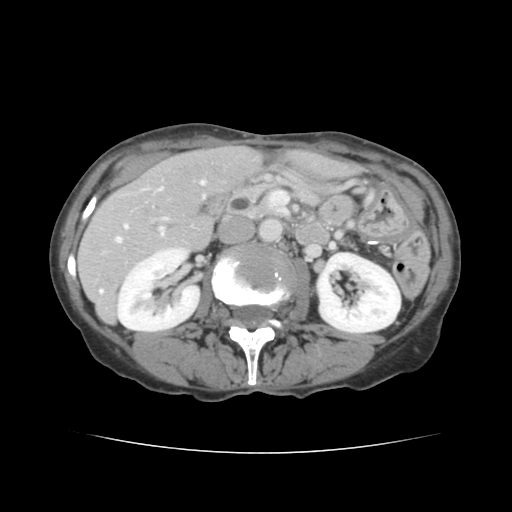
Contrast-enhanced abdominal CT, one axial slice. Position 60 of 136 along the scan axis. Intravenous contrast given. Soft-tissue window (W 400 / L 40 HU). 512 × 512 image matrix. Female patient, age 77 years. From the clinical record (not read from this slice): diagnosis: colorectal cancer liver metastases, imaged before liver resection; multiple liver metastases: yes; largest metastasis: 3 cm; disease in both lobes: no.
Structures marked on this image (outlined manually by an expert reader):
- hepatic veins: bounding box (x1, y1, x2, y2) in pixels: (116, 181, 205, 242)
- liver: (79, 146, 261, 321)
- planned liver remnant (the part of the liver to remain after resection): (164, 146, 261, 201)
- portal vein (with intrahepatic branches): (100, 227, 165, 292)